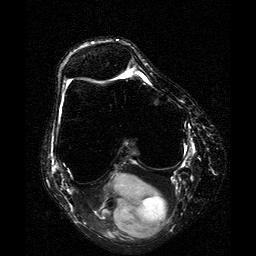
MRI of an extremity soft-tissue mass, one axial slice; T2-weighted fat-saturated; 256 × 256 image matrix. Female patient. Case-level facts recorded for this patient, not image findings: histological type: liposarcoma; site of the primary tumour: right thigh.
Annotated regions visible in this slice (manually delineated by an expert):
- gross tumour volume (mass): bounding box [x1, y1, x2, y2] px = [95, 173, 168, 239]